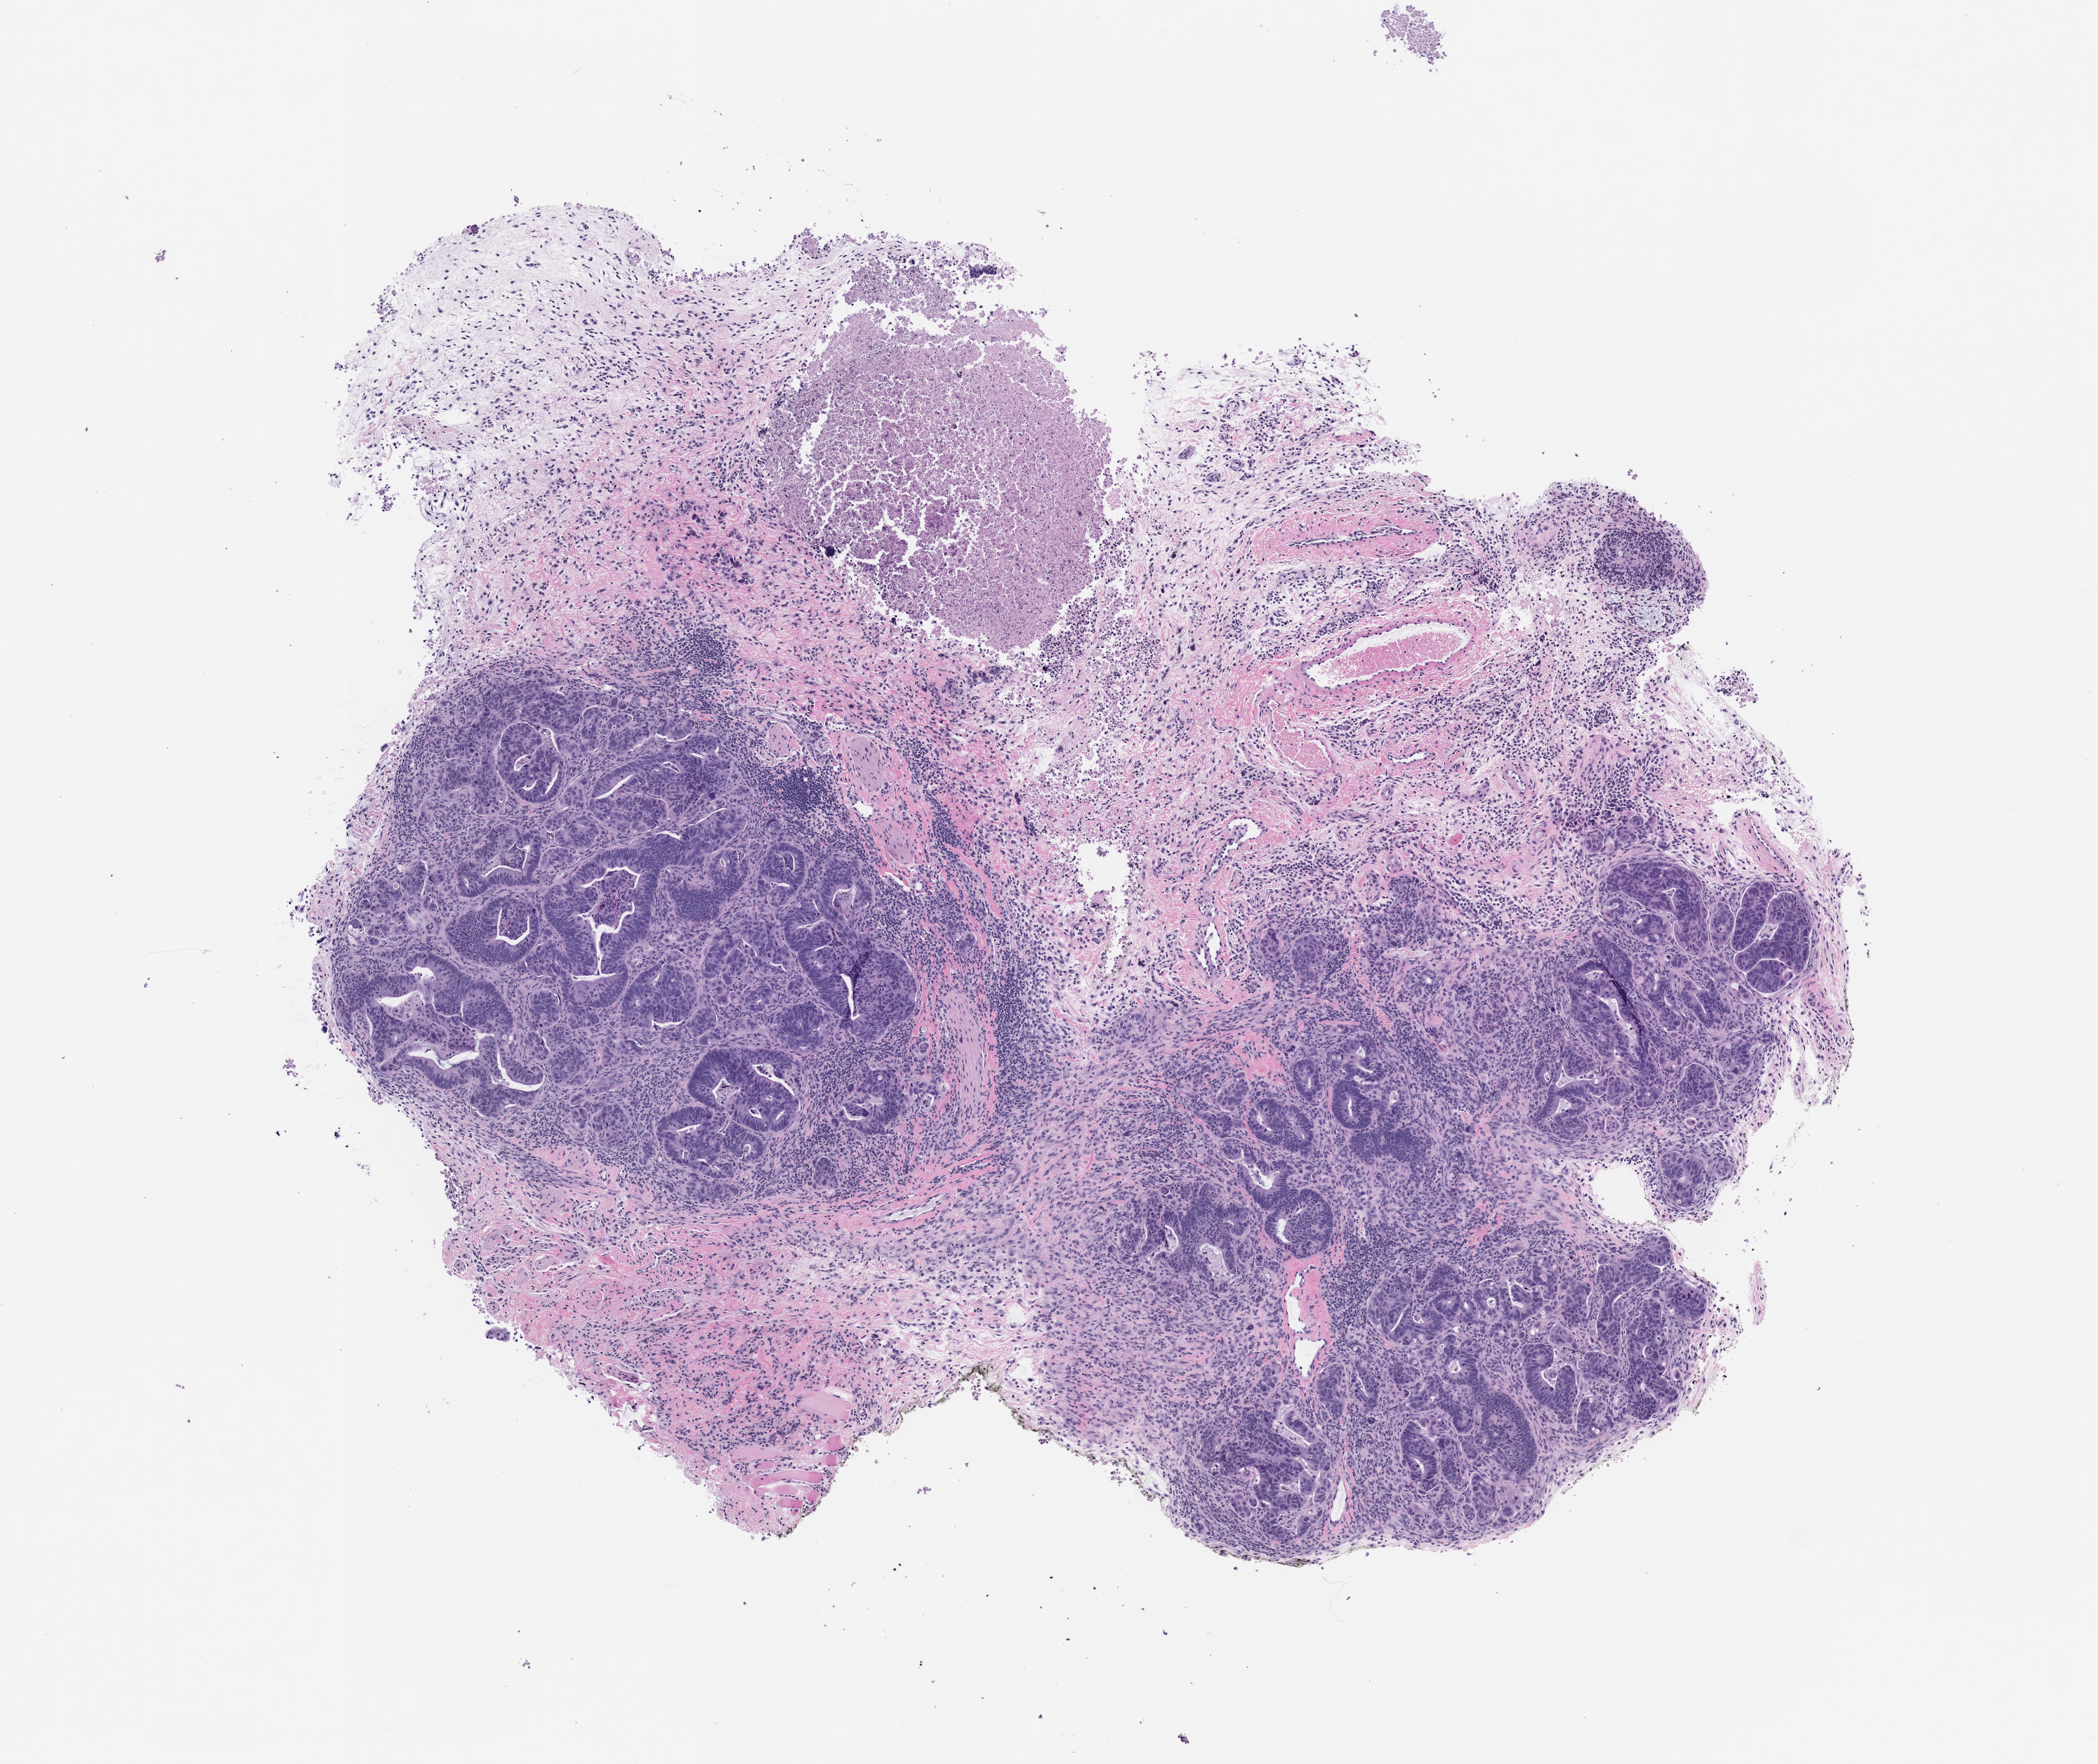
Whole-slide image, H&E: patient-derived xenograft (human tumor grown in a mouse), passage 1 — low-resolution overview of the scanned area, about 6.0 x 5.1 mm, formalin-fixed paraffin-embedded section, originating tumor site category: rectum.
Originating patient diagnosis: Rectal Adenocarcinoma.